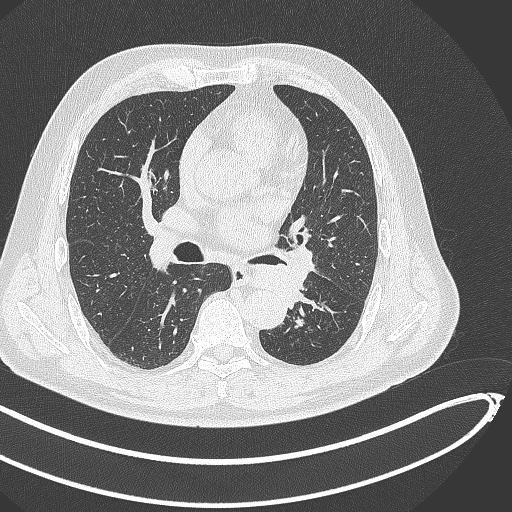
Chest CT, one axial slice; position 256 of 468 along the scan axis; reconstruction kernel B70f; lung window (W 1500 / L -600 HU); 512 × 512 image matrix, field of view 400 × 400 mm. Patient: male, 64 years. Case-level facts recorded for this patient, not image findings: clinical TNM (as recorded): T1c N0 M0.
Annotated regions visible in this slice (rectangle marked by the reading radiologist):
- lung tumour (recorded histology: squamous cell carcinoma): bounding box [x1, y1, x2, y2] px = [253, 262, 312, 311]